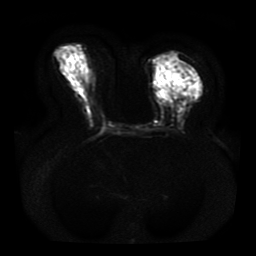
Breast MRI, one axial slice; position 19 of 41 along the scan axis; diffusion-weighted series; image 2 of 4 stored at this slice position (different b-values; order by instance number); 1.5 T; 5 mm slice thickness; 256 × 256 image matrix, field of view 330 × 330 mm. Female patient.
Annotated regions visible in this slice (expert manual segmentation):
- tumour on diffusion-weighted imaging: bounding box <178,81,193,89> (left, top, right, bottom; pixels)